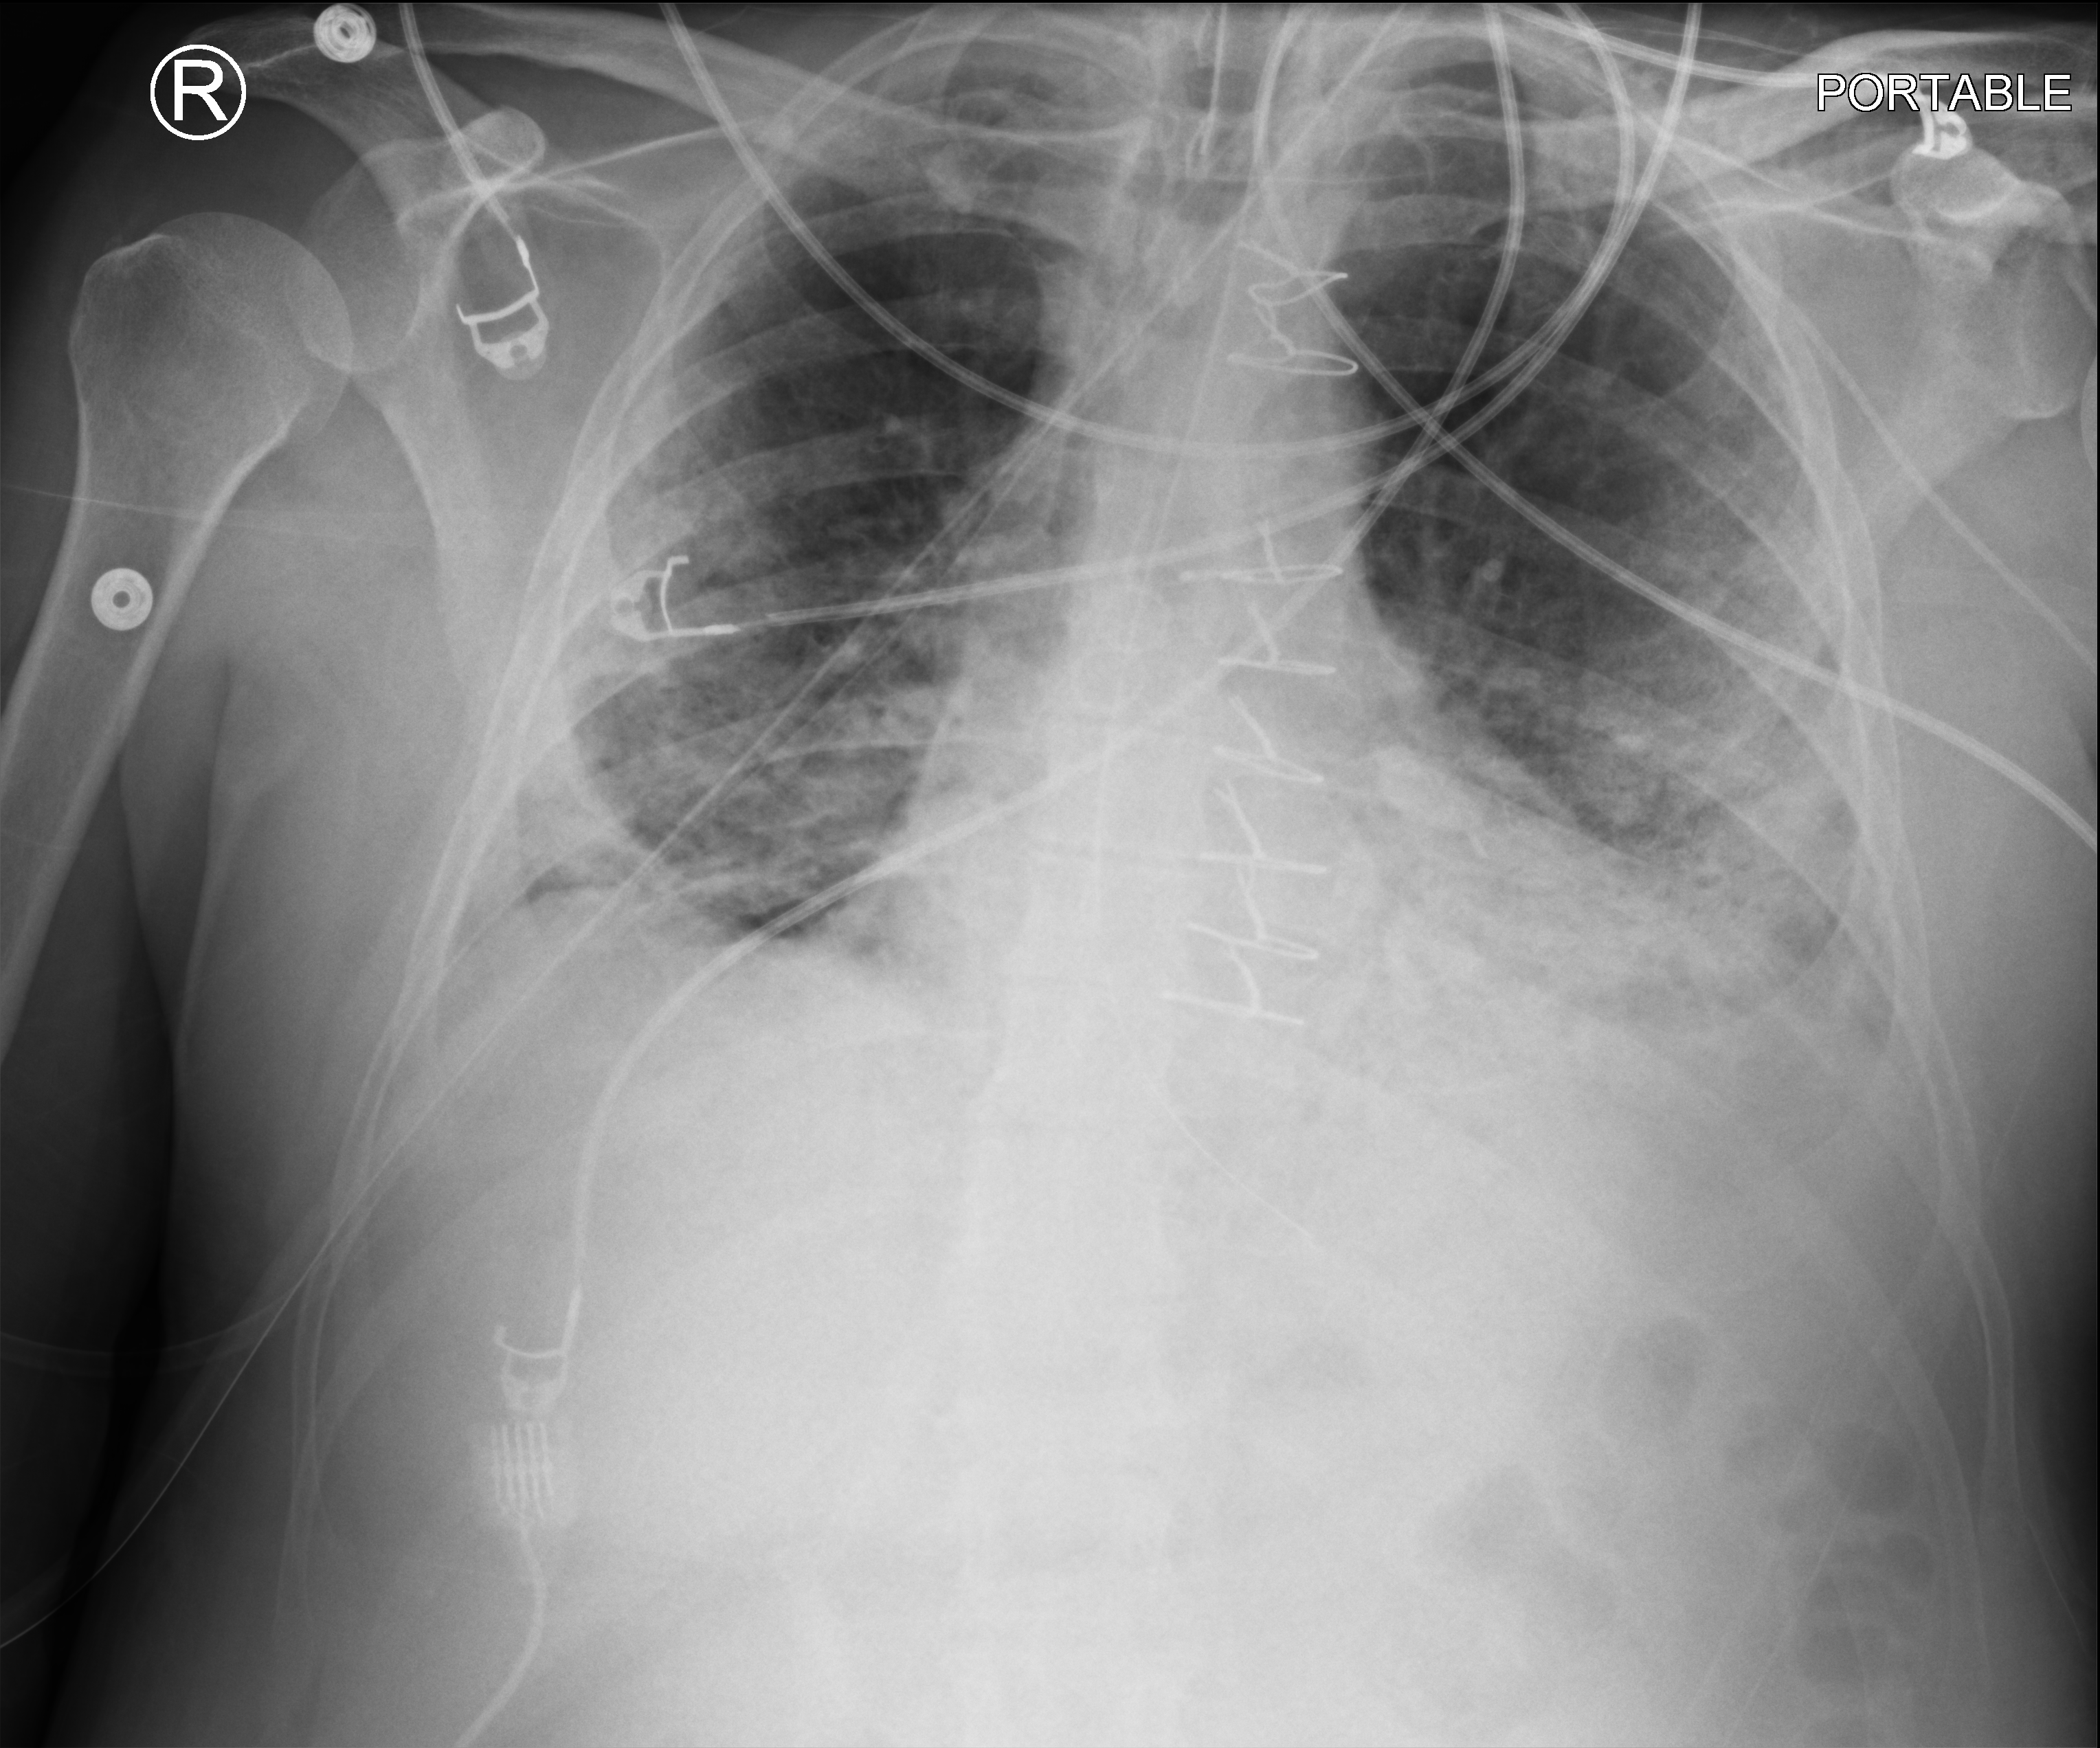
Portable chest radiograph. Male patient hospitalised with COVID-19, age 18–59 years.
Admission-level facts for this patient (not findings on this image; timing relative to this image not recorded): length of hospital stay: 63 days.